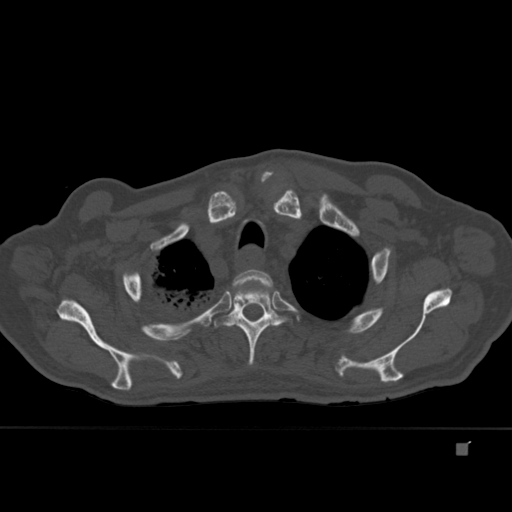
CT including the spine, one axial slice. Slice 336 of 451 in the series (ordered by position). Bone window (W 1800 / L 400 HU). 1.5 mm slice thickness. 512 × 512 image matrix, field of view 378 × 378 mm. Patient: male, 75 years. From the clinical record (not read from this slice): primary cancer: prostate.
Annotated regions visible in this slice (semi-automatic segmentation, software-assisted and operator-edited):
- T2 vertebra: box from (x=226, y=269) to (x=280, y=307) px
- T3 vertebra: (x=214, y=284)–(x=289, y=365)